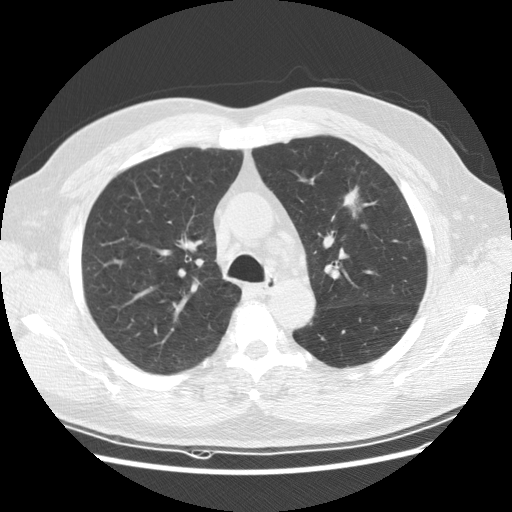
Low-dose screening chest CT, axial slice; baseline annual screen; lung window (W 1500 / L -600 HU); 2.5 mm slice thickness. Male participant, aged 65 years at enrolment. Current smoker at enrolment.
Expert reader's lesion annotation, box from (x=323, y=180) to (x=380, y=231) px. The screening reader recorded 2 non-calcified nodules or masses ≥4 mm on this exam (left upper lobe, right upper lobe); which of them this box marks is not recorded. Official screen result: positive, change unspecified: nodule(s) >= 4 mm or enlarging nodule(s), mass(es), or other non-specific abnormalities suspicious for lung cancer. Later outcome: lung cancer diagnosed 488 days after this screen — carcinoma, NOS, left upper lobe, poorly differentiated (G3), stage IIIA (AJCC 6th edition), 25 mm at pathology.